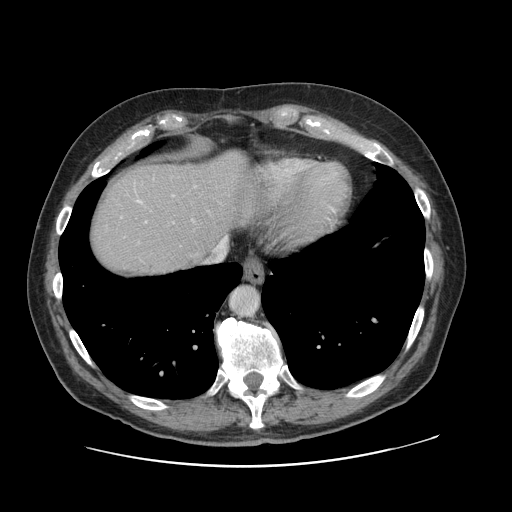
Contrast-enhanced abdominal CT, one axial slice. Position 105 of 138 along the scan axis. 120 kVp. Intravenous contrast given. Soft-tissue window (W 400 / L 40 HU). 2.5 mm slice thickness. 512 × 512 image matrix. Male patient, age 71 years. From the clinical record (not read from this slice): diagnosis: colorectal cancer liver metastases, imaged before liver resection; multiple liver metastases: no; largest metastasis: 3.3 cm.
Outlined on this slice (expert manual segmentation):
- hepatic veins: bounding box (x1, y1, x2, y2) in pixels: (204, 236, 227, 264)
- liver: (89, 150, 255, 278)
- planned liver remnant (the part of the liver to remain after resection): (90, 164, 227, 278)